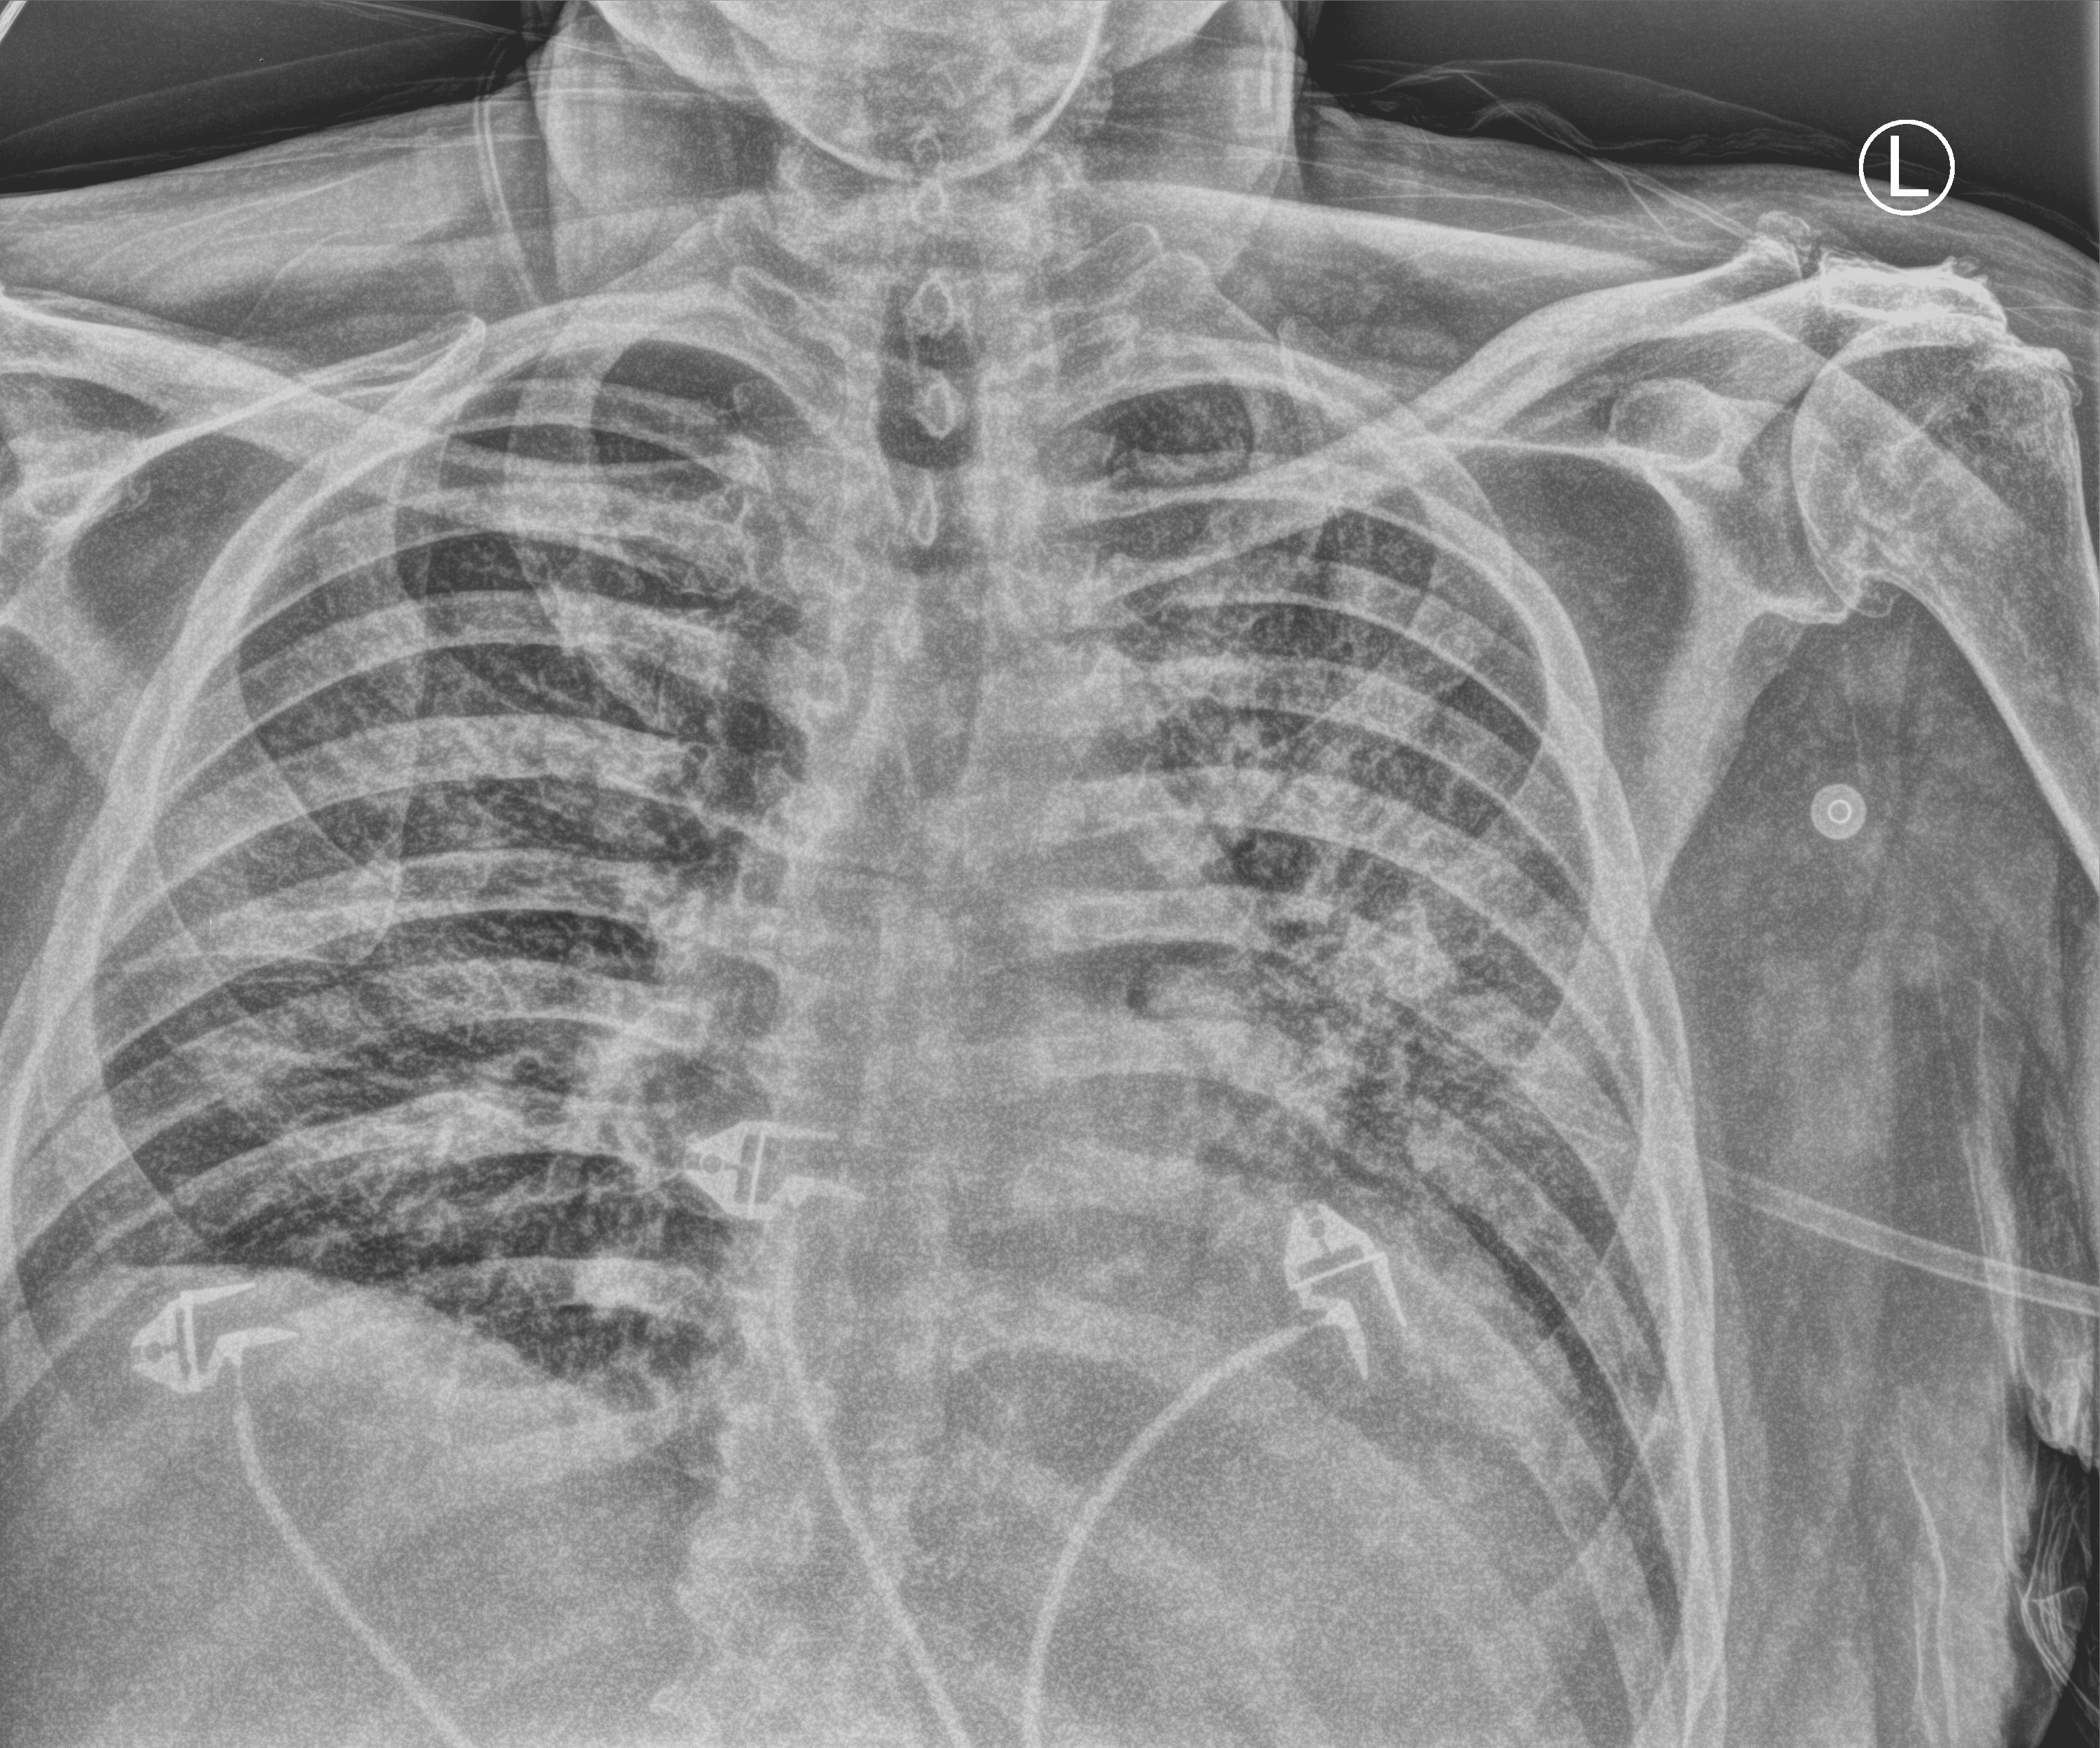
Bedside chest radiograph (computed radiography), anteroposterior (AP) projection. Patient hospitalised with COVID-19; male, aged 60–74 years.
From the hospital-stay record, not from the radiograph (when in the stay this image was taken is not recorded):
- mechanically ventilated during this hospital stay: yes
- admitted to intensive care during this hospital stay: yes